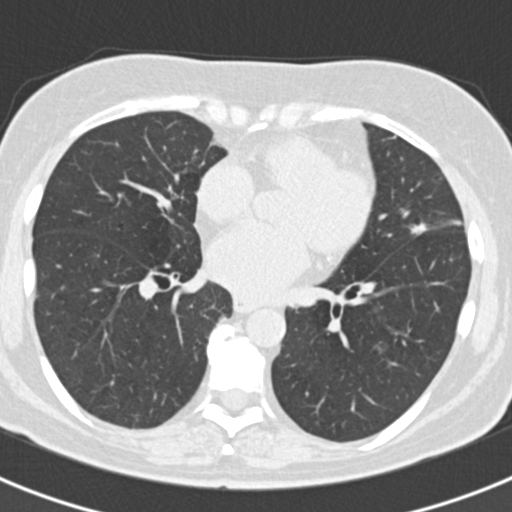
Chest CT (low-dose screening protocol), one axial image. First (baseline) screen. Lung window (W 1500 / L -600 HU). 2 mm slice thickness. 512 × 512 image matrix. Female participant, aged 60 years at enrolment. Current smoker at enrolment.
Expert reader's lesion annotation, bounding box <399,215,437,248> (left, top, right, bottom; pixels). The screening reader recorded 3 non-calcified nodules or masses ≥4 mm on this exam (lingula, left lower lobe, lingula); which of them this box marks is not recorded. Lung cancer was diagnosed 886 days after this screen: non-small cell carcinoma, left upper lobe, poorly differentiated (G3), stage IB (AJCC 6th edition), 7 mm at pathology.